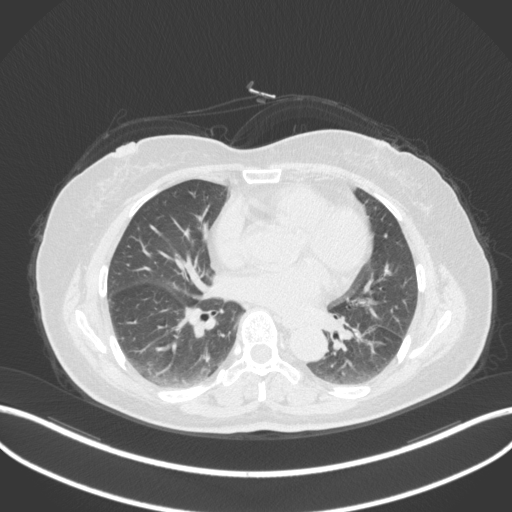
Chest CT, one axial slice. Position 172 of 307 along the scan axis. Reconstruction kernel B31f. Lung window (W 1500 / L -600 HU). 512 × 512 image matrix, field of view 400 × 400 mm. Female patient, age 59 years. From the clinical record (not read from this slice): clinical TNM (as recorded): T2a N0 M0.
Annotated regions visible in this slice (bounding box drawn by a radiologist):
- lung tumour (recorded histology: adenocarcinoma): bounding box [x1, y1, x2, y2] px = [349, 322, 390, 361]